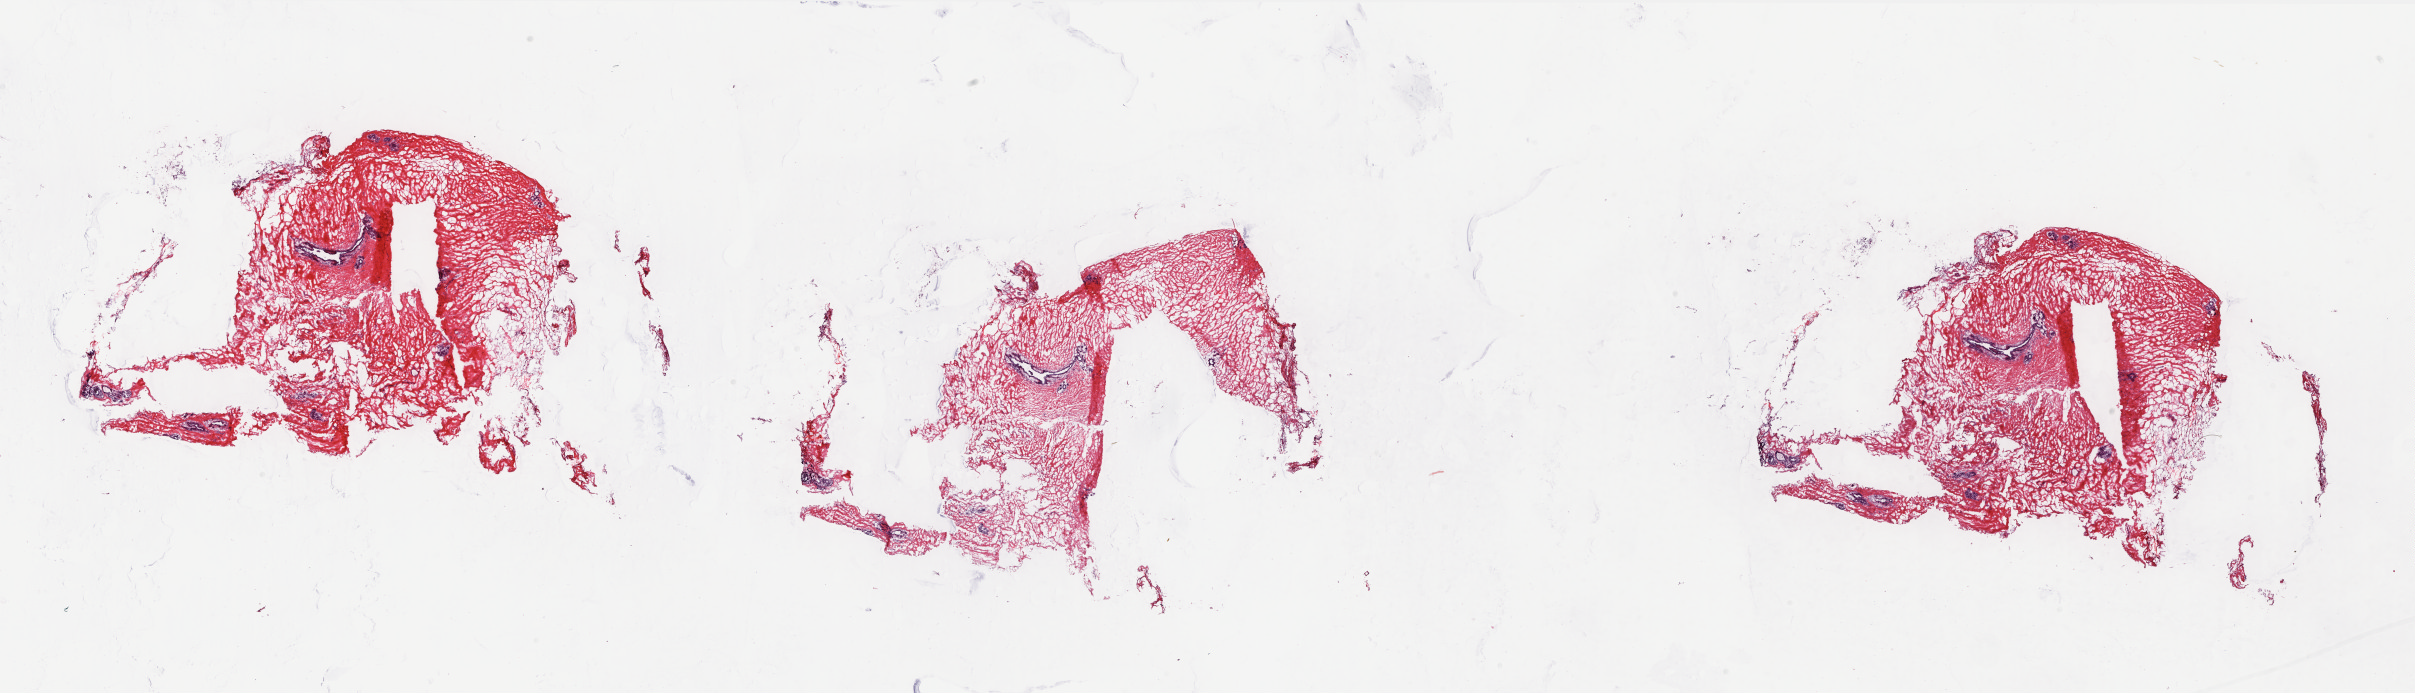
Digitized H&E tissue section (whole slide), low-resolution overview of the scanned area, about 39.0 x 11.2 mm (from a 20x scan), frozen section, breast, solid tissue normal (non-tumour tissue) sample. Female, age 48 years at initial diagnosis. Composition of this section per pathologist review: tumour cells 0%, tumour nuclei 0%, normal cells 90%, stromal cells 10%, necrosis 0%. Infiltration values recorded for this section: lymphocyte infiltration 70%, monocyte infiltration 10%, neutrophil infiltration 10%.
This section: solid tissue normal (non-tumour) sample from the same patient. Patient diagnosis: Lobular carcinoma, NOS.